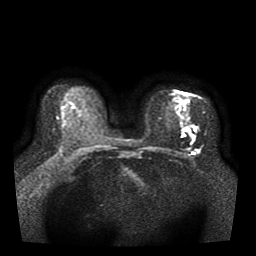
Breast MRI, one axial slice; position 22 of 41 along the scan axis; diffusion-weighted series; image 2 of 4 stored at this slice position (different b-values; order by instance number); 1.5 T; 5 mm slice thickness; 256 × 256 image matrix, field of view 330 × 330 mm. Female patient.
Annotated regions visible in this slice (expert manual segmentation):
- tumour on diffusion-weighted imaging: bounding box (x1, y1, x2, y2) in pixels: (181, 101, 195, 139)